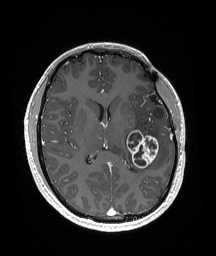
Brain MRI from a brain-tumour surgery series, one axial slice. Slice 84 of 192 in the series (ordered by position). T1-weighted post-contrast. 1 mm slice thickness. 216 × 256 image matrix, field of view 211 × 250 mm. From the clinical record (not read from this slice): histopathology: Glioneuronal tumor; WHO grade: 2; tumour location: Left Superior Temporal Gyrus.
Annotated regions visible in this slice (expert manual segmentation):
- tumour: bounding box <126,129,159,168> (left, top, right, bottom; pixels)